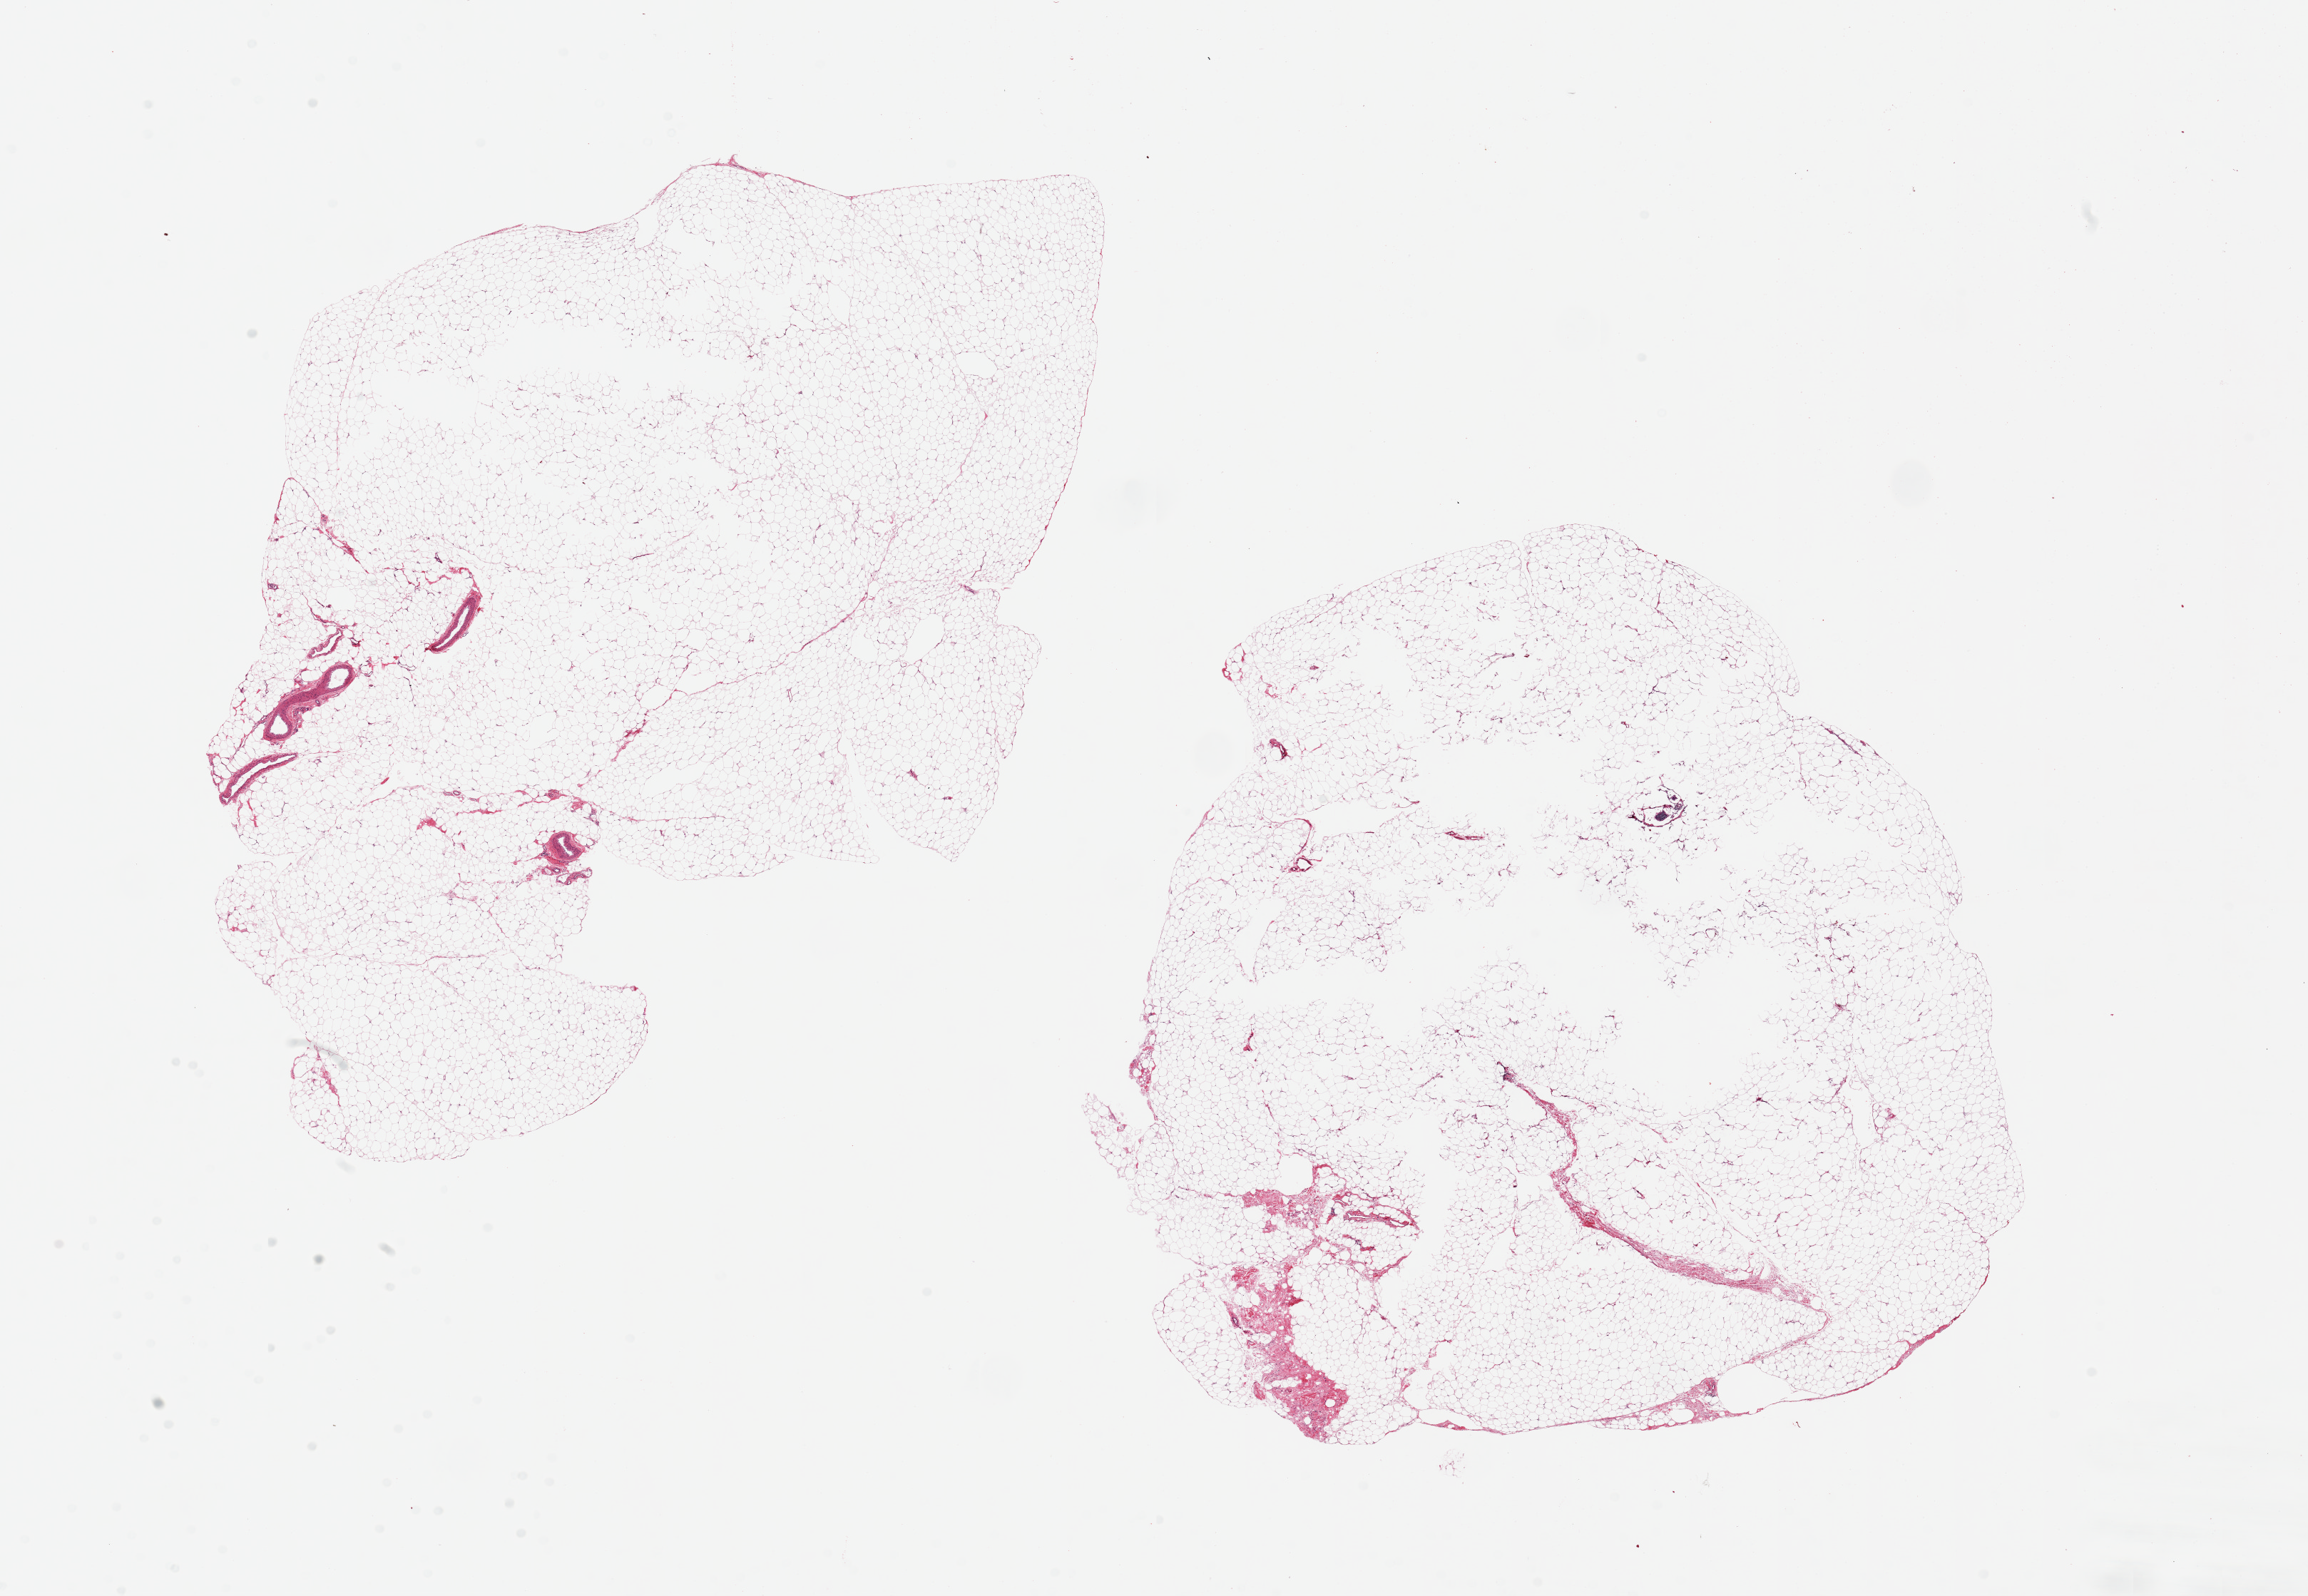
Hematoxylin and eosin (H&E) whole-slide image, low-resolution overview of the scanned area, about 25.6 x 17.7 mm (from a 20x scan). PAXgene-fixed paraffin-embedded (PFPE) section. Target tissue: omentum. Tissue donor sample. Donor sex: male.
* pathologist's review note for this sample: 2 pieces ~12x8mm